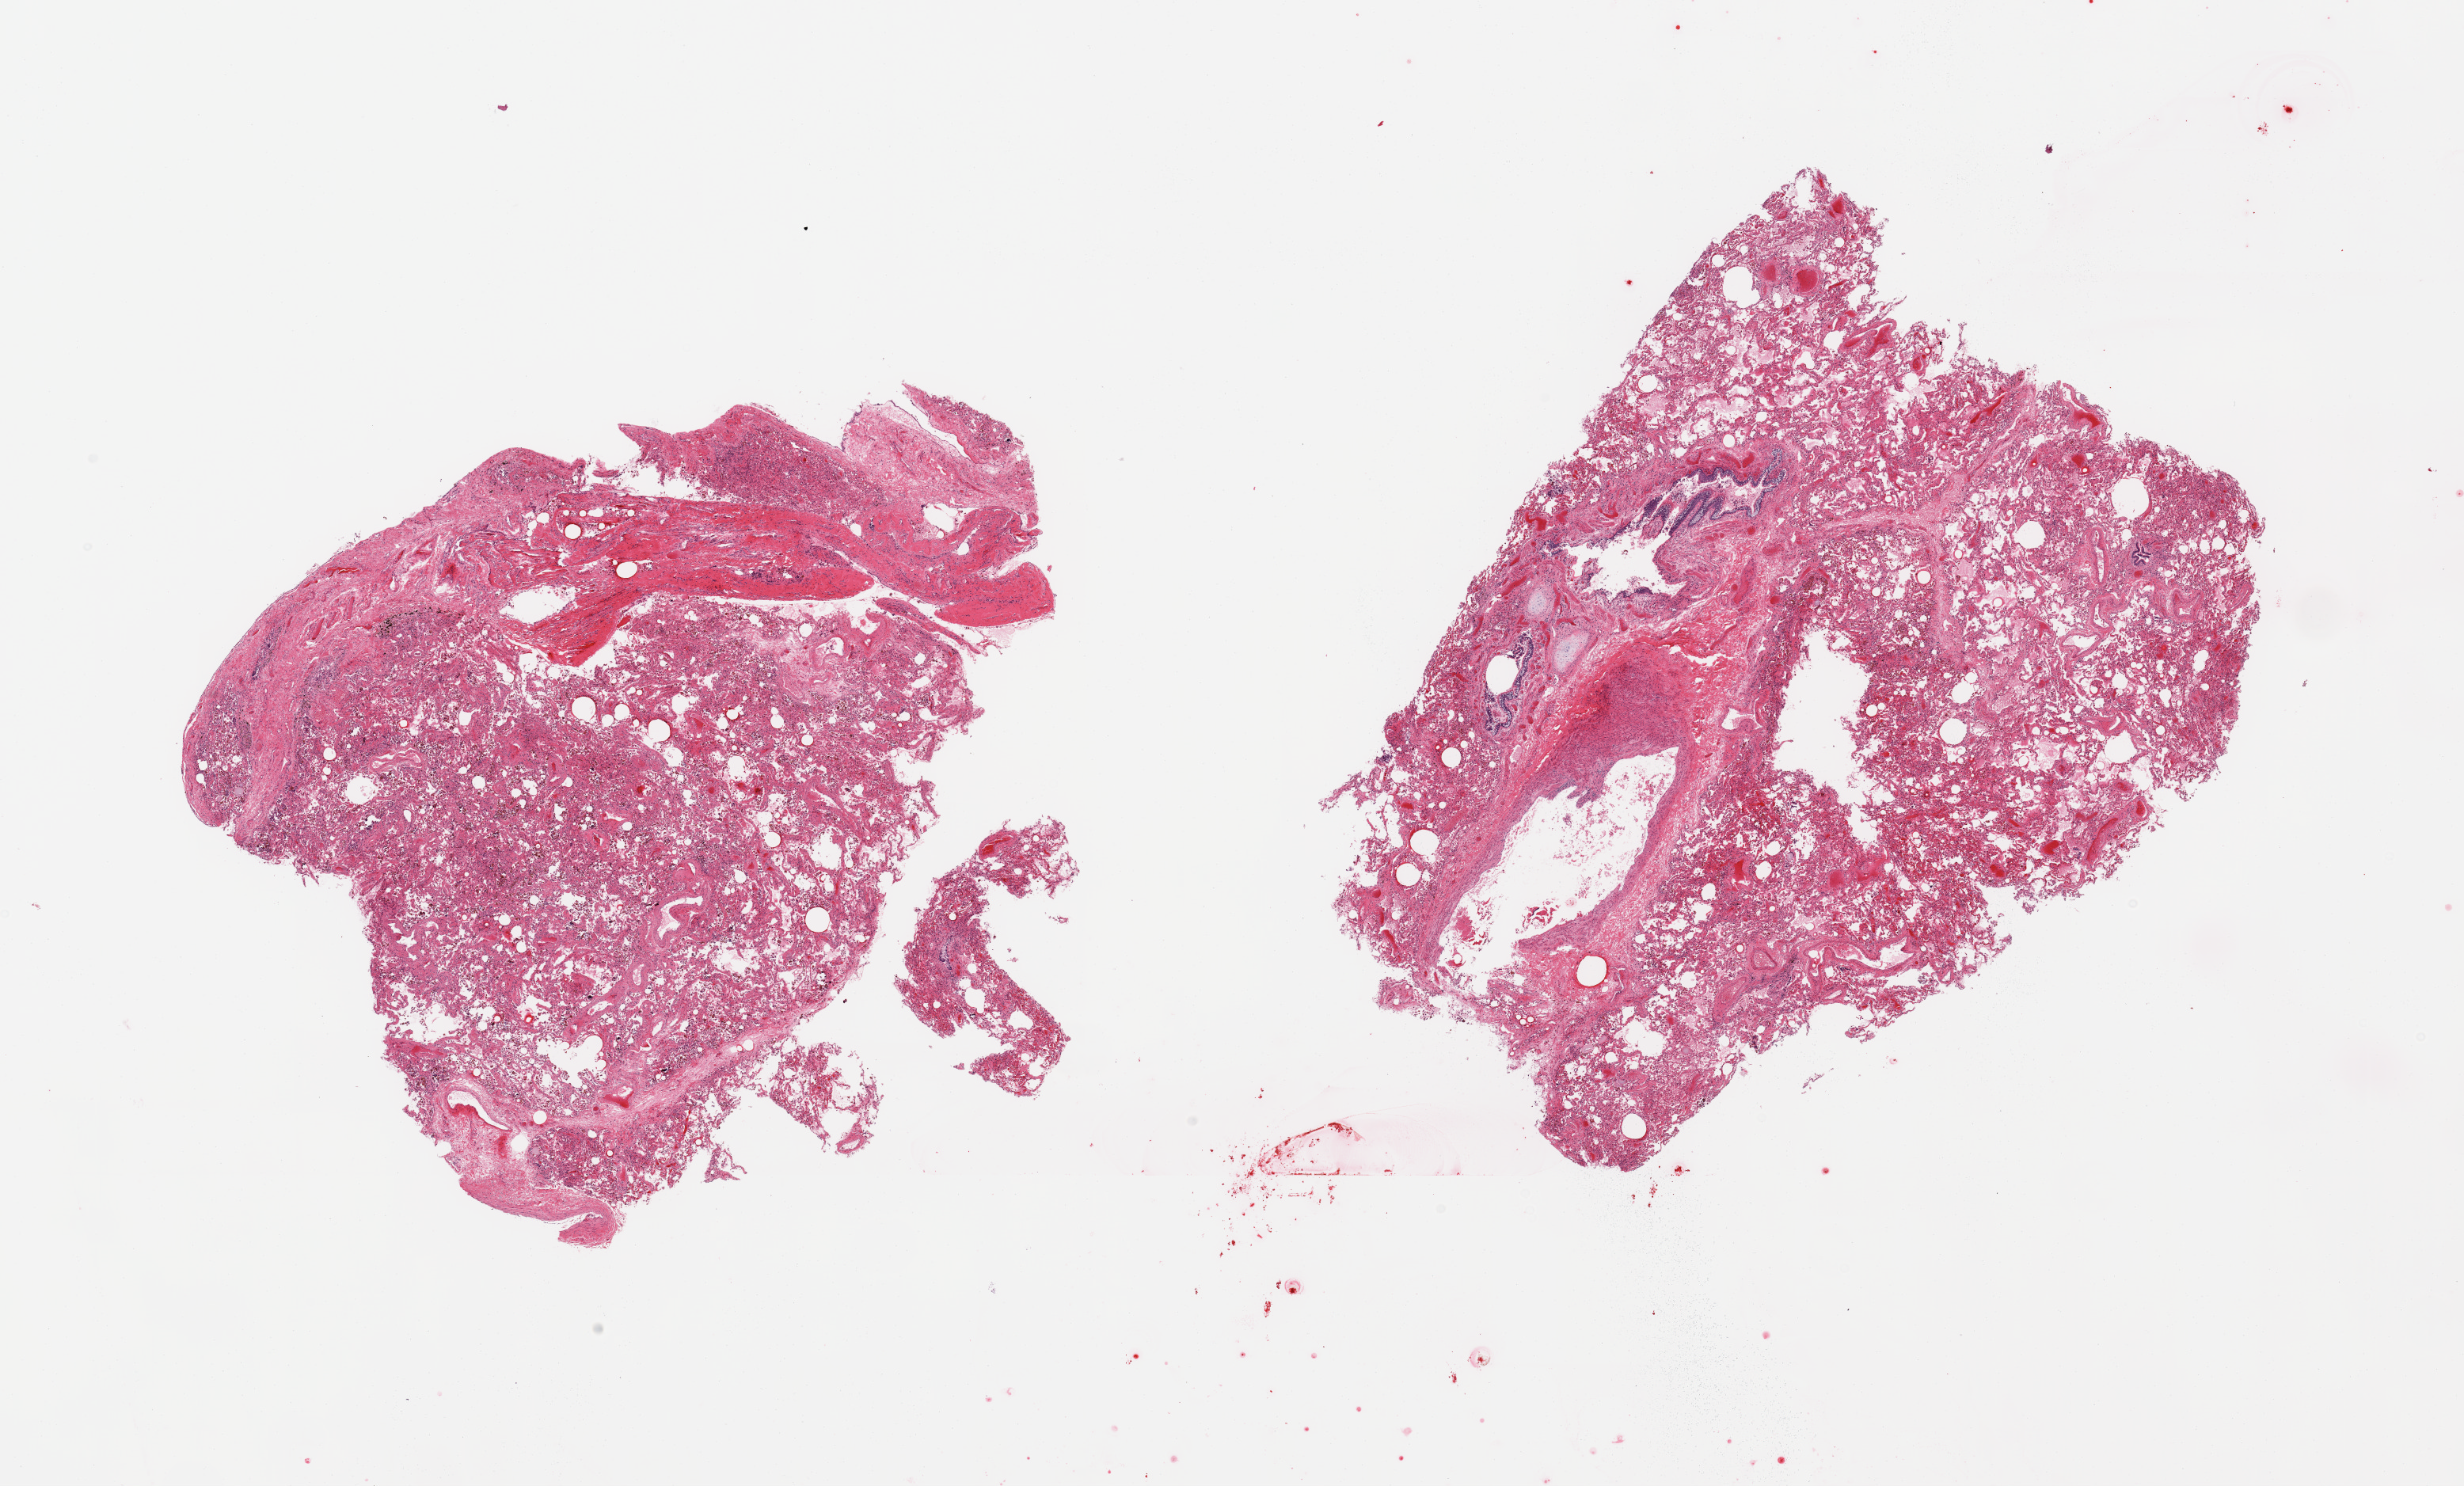
Whole-slide image, H&E stain, whole scanned area (about 24.6 x 14.8 mm, slide scanned at 20x) shown as a low-resolution overview; PAXgene-fixed paraffin-embedded (PFPE) section; sampled site (target tissue): lung; tissue donor sample. Donor sex: male.
• pathologist's review note for this sample: 2 pieces, moderate congestion